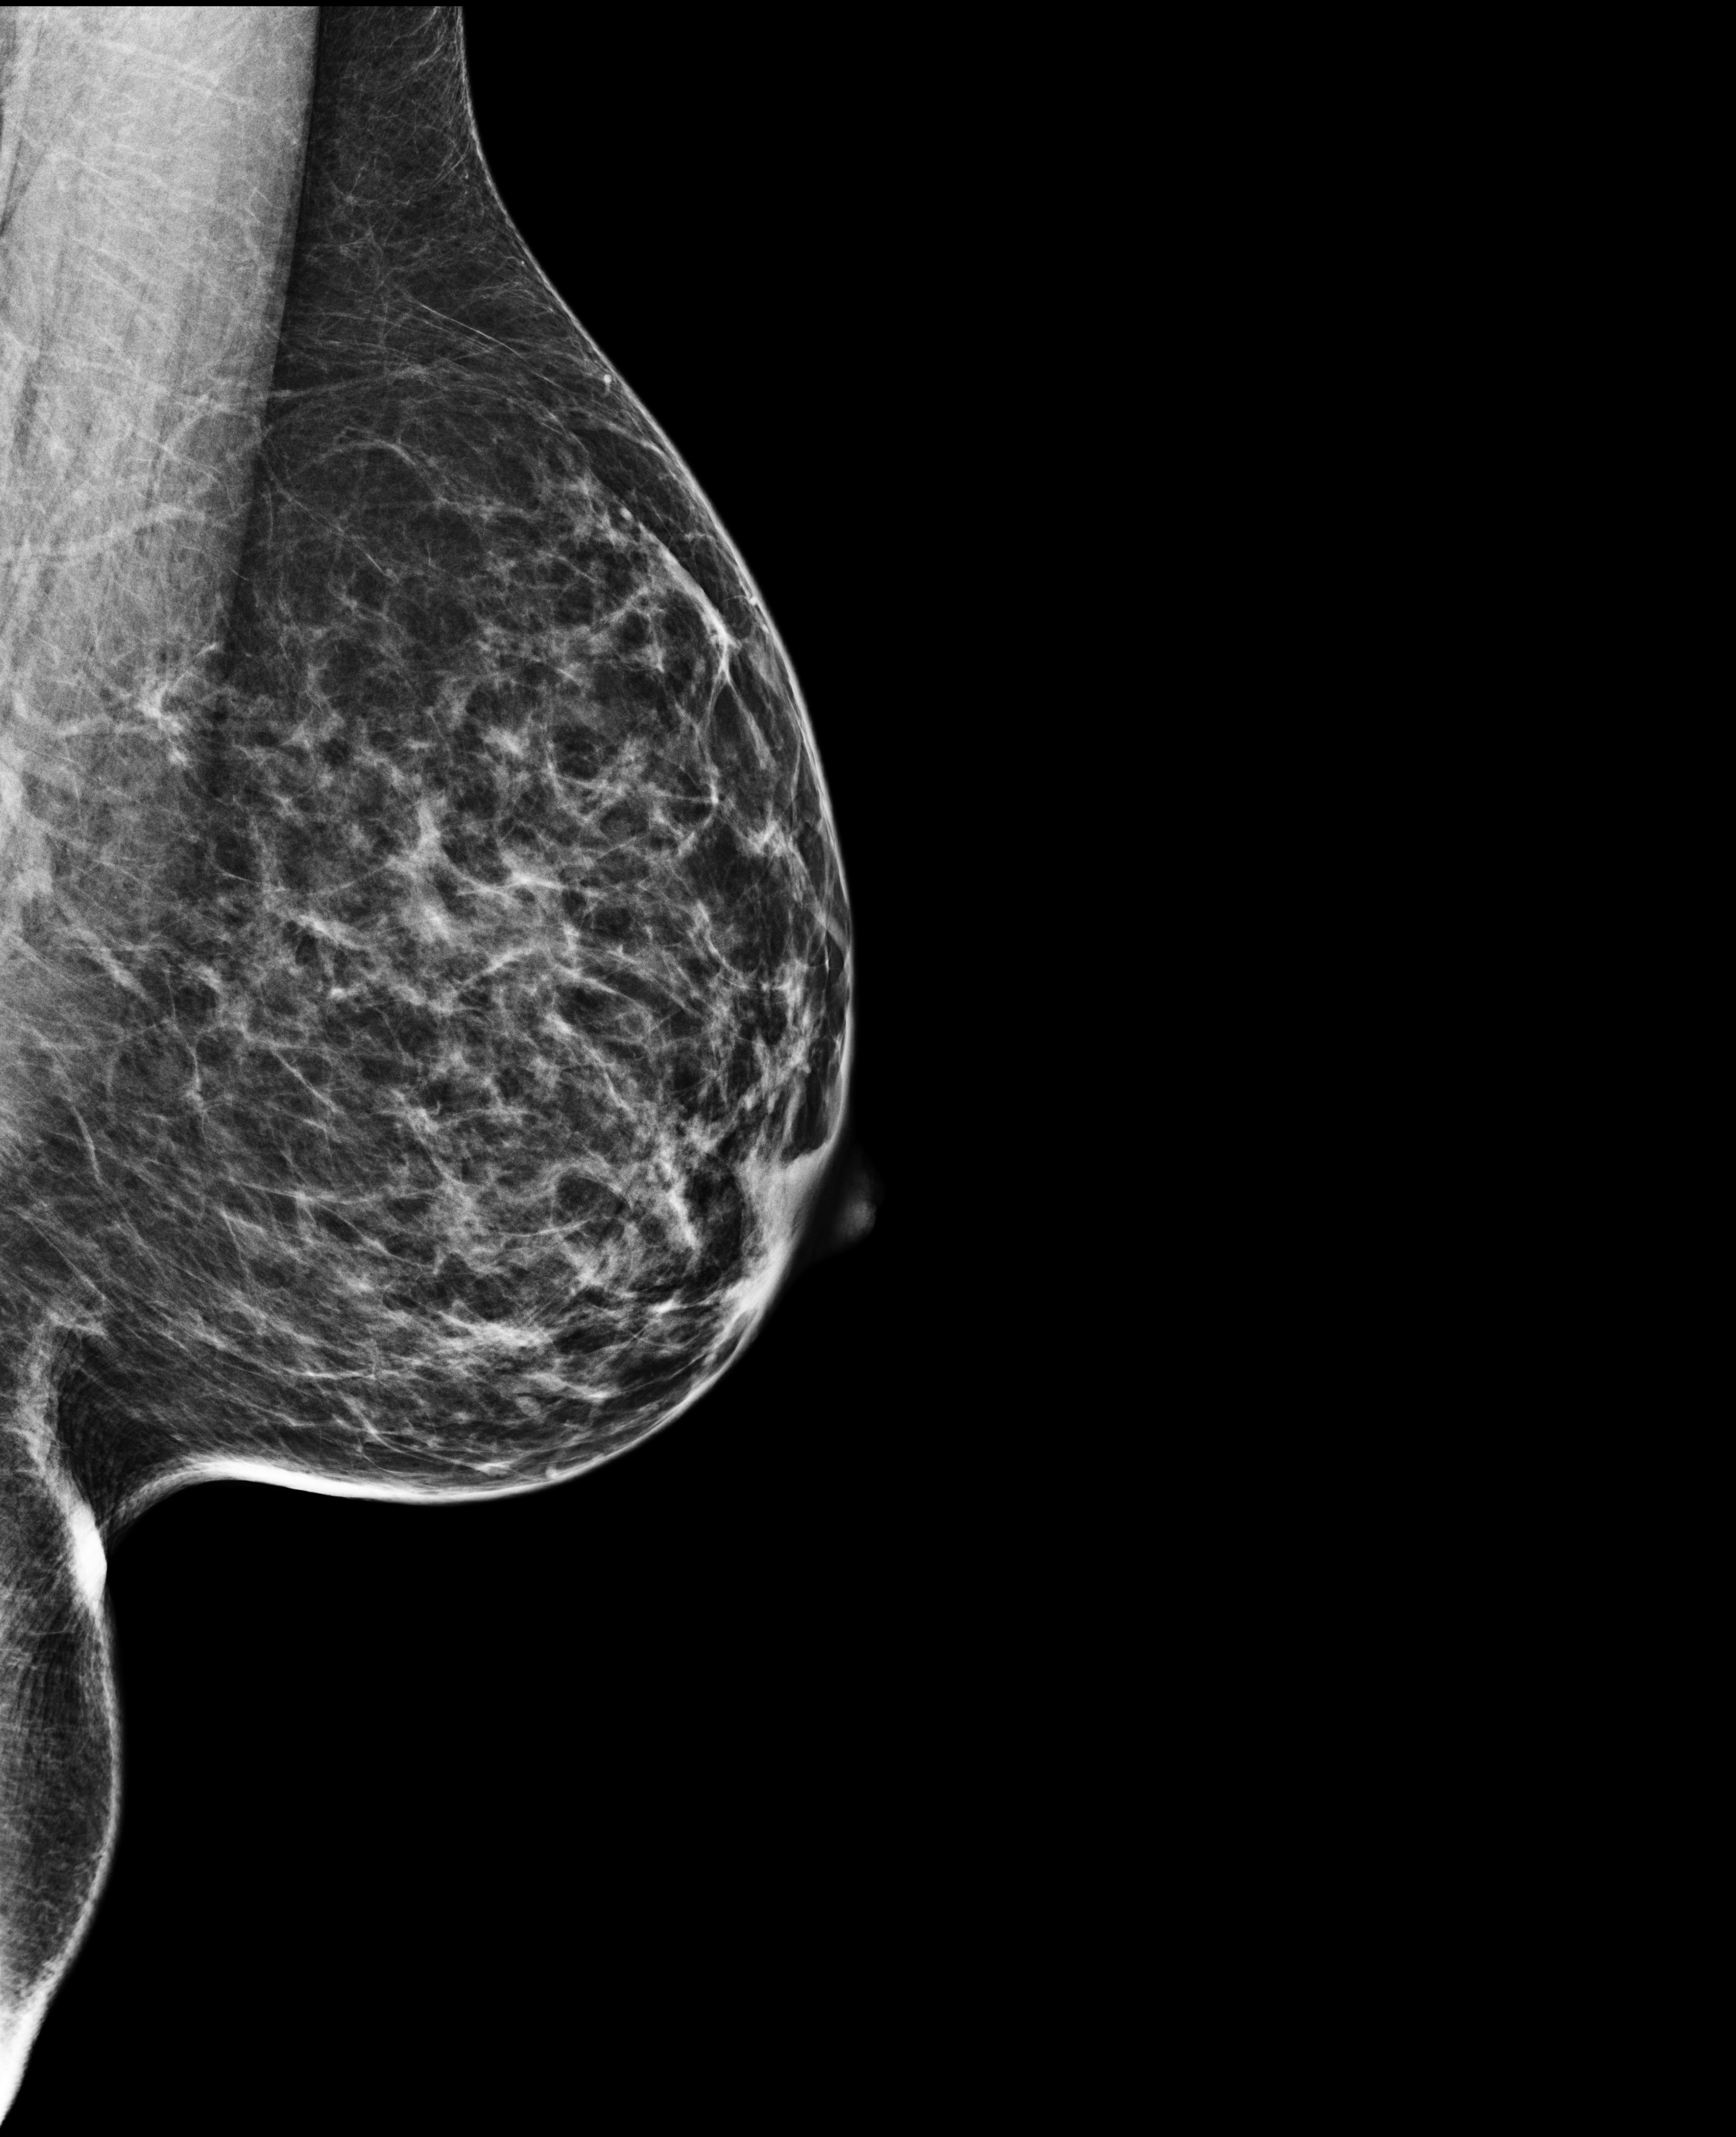
Full-field digital mammogram (FFDM), left breast, mediolateral oblique (MLO) view, annual screening mammography examination, system: Selenia Dimensions. Patient aged 48 years (female).
Breast density at the screening exam (both breasts): scattered fibroglandular densities (BI-RADS density category b). Final BI-RADS category for the screening round (tomosynthesis exam, both breasts): category 1. Recall: no recall after this screen.